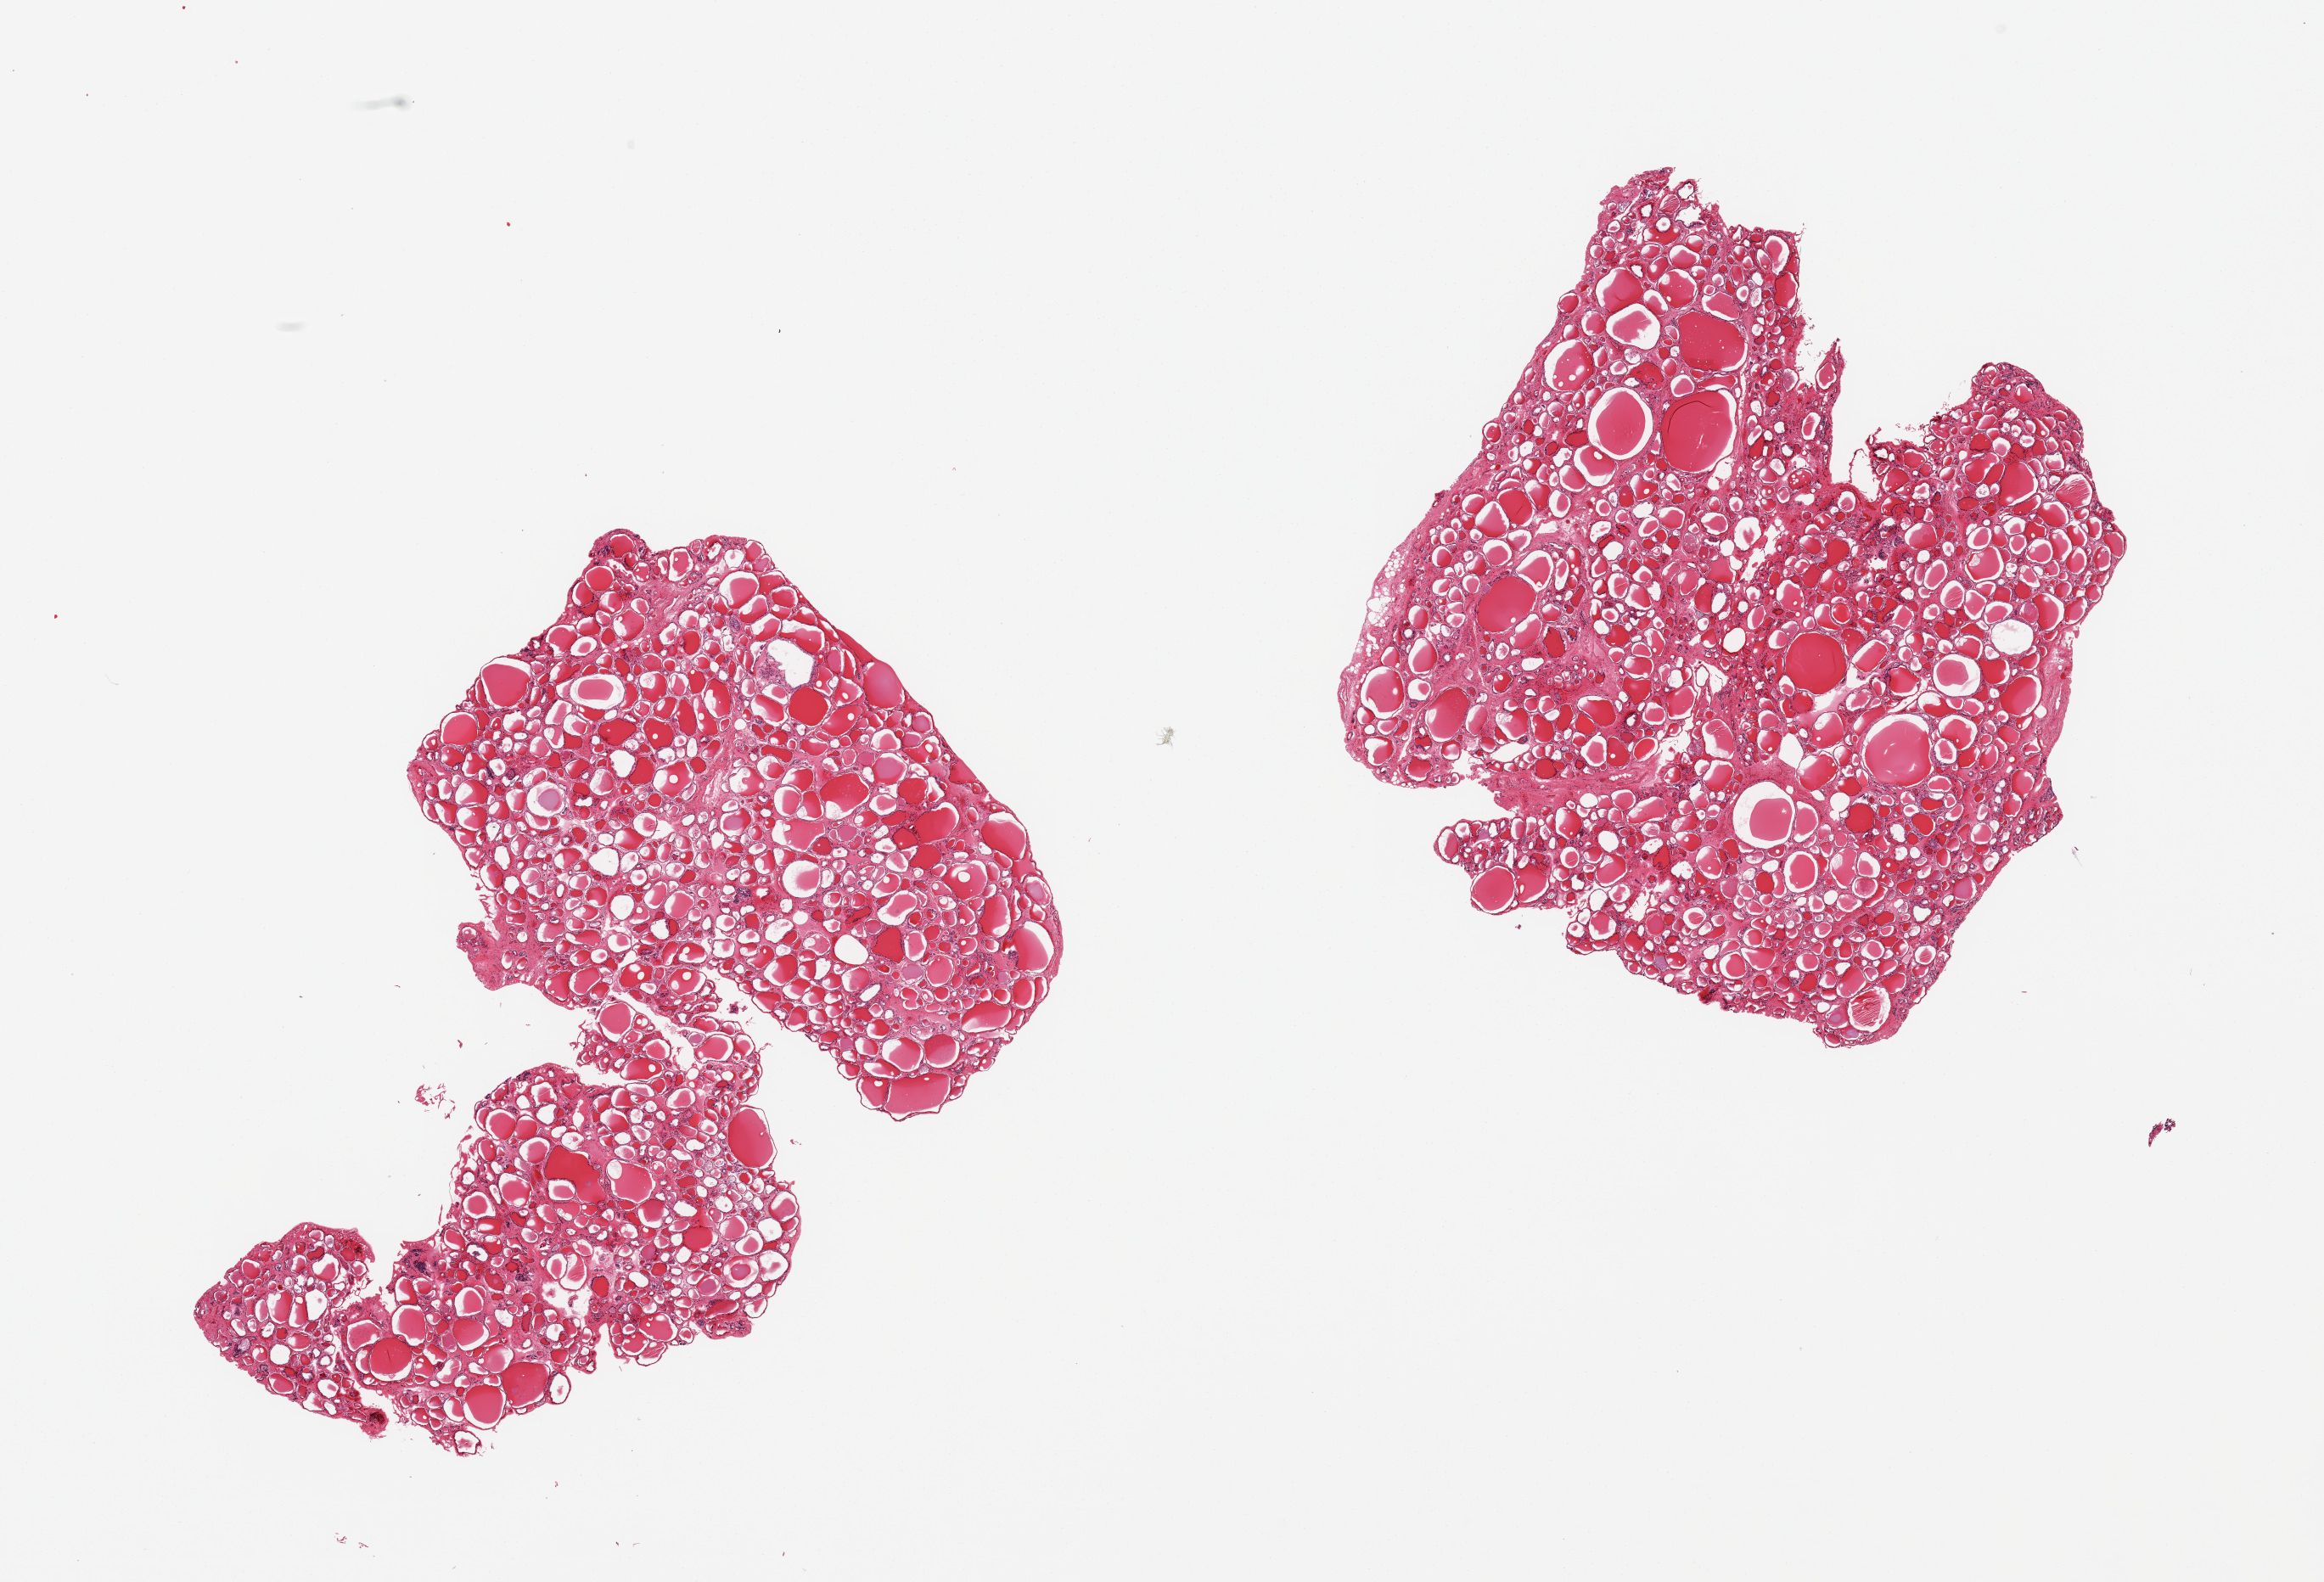
H&E whole-slide image — a low-resolution overview of the entire scanned area, about 21.7 x 14.7 mm. PAXgene-fixed, paraffin-embedded tissue. Target tissue: thyroid. Tissue donor sample. Male donor.
Reviewer comment on this tissue sample: 2 pieces, no abnormalities.